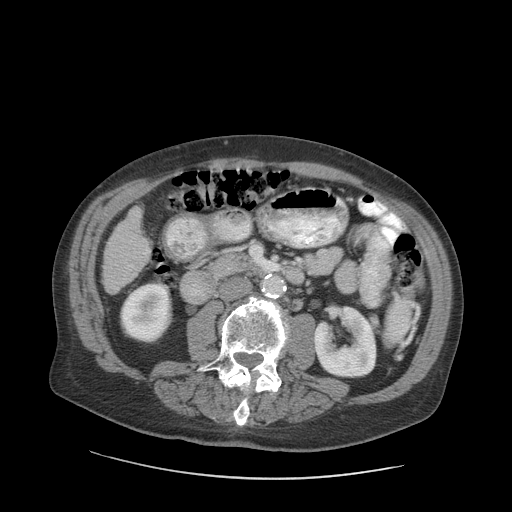
Contrast-enhanced abdominal CT (liver protocol), one axial slice. Slice 27 of 89 in the series (ordered by position). 140 kVp. Soft-tissue window (W 400 / L 40 HU). 2.5 mm slice thickness. 512 × 512 image matrix. Case-level facts recorded for this patient, not image findings: diagnosis: hepatocellular carcinoma (patient treated with transarterial chemoembolisation; whether this scan precedes or follows treatment is not stated here); TNM stage (as recorded): Stage-I; Child-Pugh class: A; tumour differentiation: moderately differentiated; tumour nodularity: uninodular.
Annotated regions visible in this slice (semi-automatically segmented with operator editing):
- liver parenchyma outside the tumour (the mass and vessels are separate outlines, so this box may not span the whole liver): box from (x=102, y=206) to (x=150, y=294) px
- liver vessels: (x=129, y=249)–(x=149, y=268)